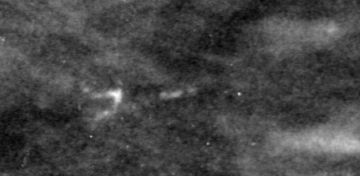
Region of interest cut from a scanned film mammogram (one marked finding); left breast; CC view.
- Calcifications, morphology fine linear branching, distribution linear; BI-RADS assessment category 4; pathology result (as recorded, not read from the image): malignant.